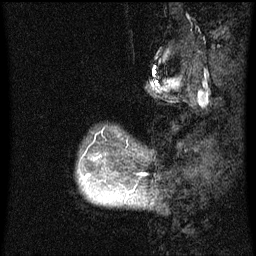
Breast MRI (dynamic contrast-enhanced), one sagittal slice; slice 10 of 60 in the series (ordered by position); dynamic contrast-enhanced series, image 2 of 3 at this slice position (ordered by acquisition); 1.5 T; TE 4.2 ms, TR 8 ms; 2 mm slice thickness; 256 × 256 image matrix, field of view 190 × 190 mm. Female patient, age 50 years.
Outlined on this slice (semi-automatic segmentation, software-assisted and operator-edited):
- analysis volume of interest (the breast-tissue region the enhancement analysis was run in; not a lesion): bounding box <79,131,142,205> (left, top, right, bottom; pixels)
- tumour enhancement mask (voxels above the 70 % enhancement threshold inside the analysis volume of interest): <83,177,128,202>